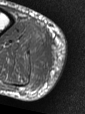
MRI of an extremity soft-tissue mass, one axial slice. Position 11 of 47 along the scan axis. MR volume resampled by the dataset authors to the PET/CT grid (not the native acquisition matrix). 3.27 mm slice thickness. 85 × 114 image matrix, field of view 83 × 111 mm. Male patient. Case-level facts recorded for this patient, not image findings: histological type: pleiomorphic liposarcoma; grade: high; site of the primary tumour: right calf.
Annotated regions visible in this slice (expert contour drawn on MRI and transferred to this co-registered scan by the dataset authors):
- gross tumour volume including surrounding oedema: box from (x=29, y=35) to (x=53, y=74) px